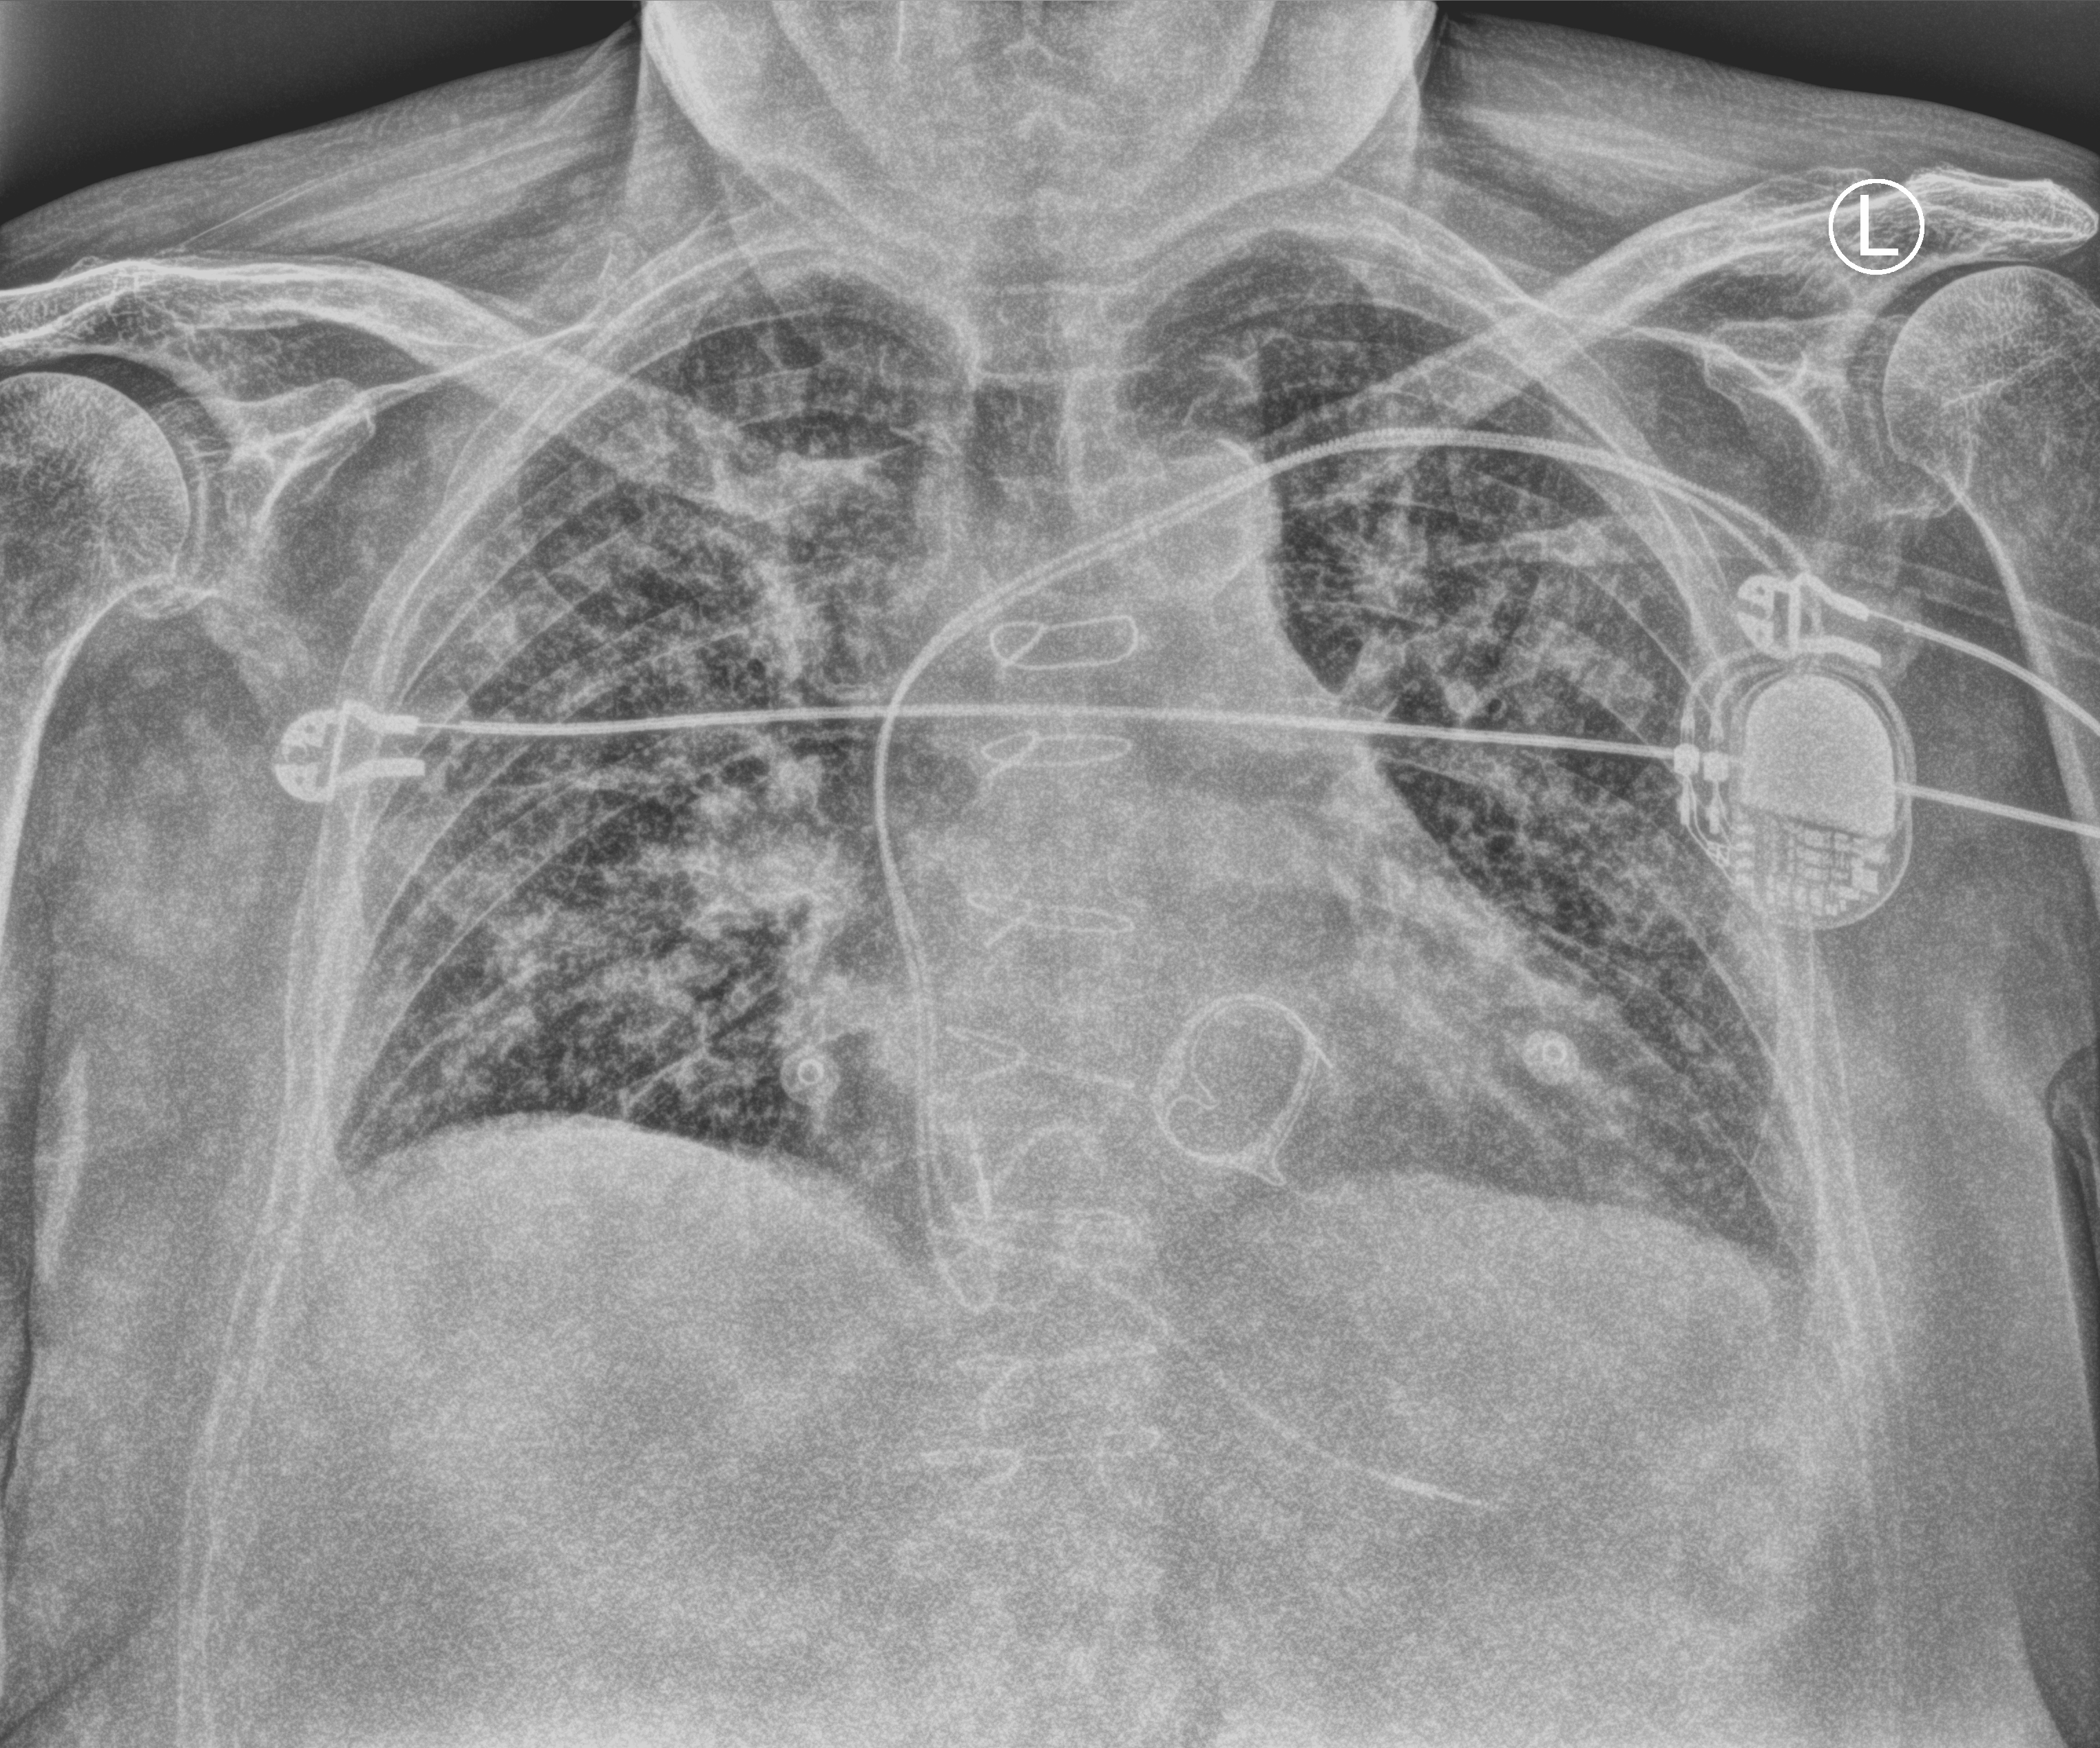
Chest X-ray (portable), anteroposterior (AP) projection. Patient hospitalised with COVID-19; male, aged 75–90 years.
From the hospital-stay record, not from the radiograph (when in the stay this image was taken is not recorded): hypertension (admission record): yes; mechanically ventilated during this hospital stay: no.